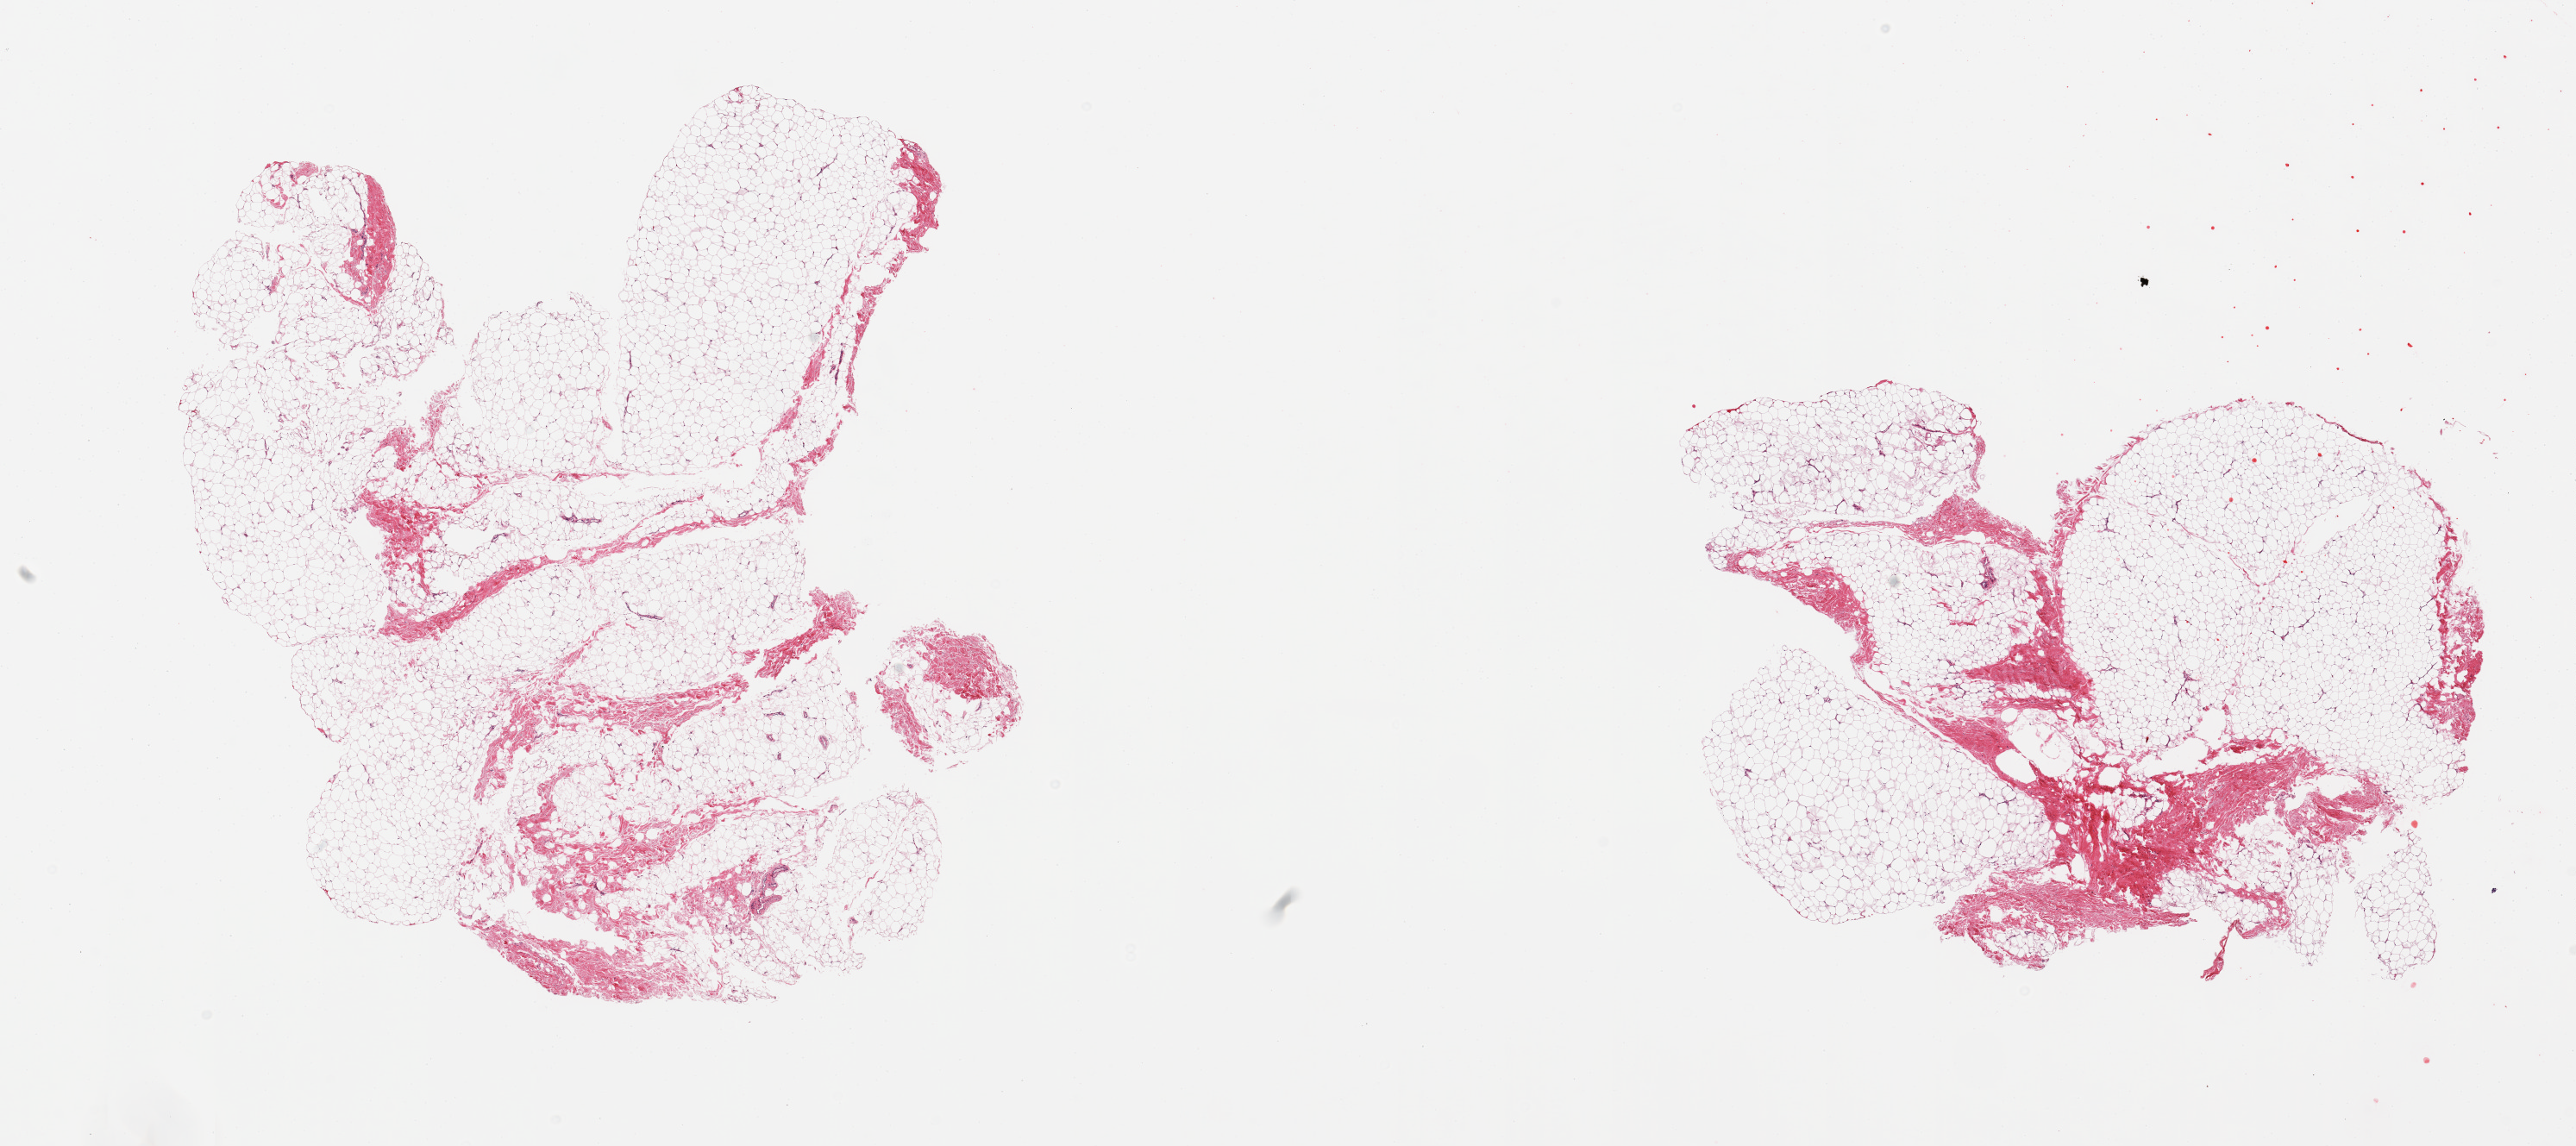
Digitized H&E-stained section — shown as a low-resolution overview of the whole scanned area (about 23.6 x 10.5 mm), PAXgene-fixed paraffin-embedded (PFPE) section, sampled site (target tissue): breast, donor tissue sample.
* pathologist's review note for this sample: 2 pieces; all fibroadipose, no mammary ducts